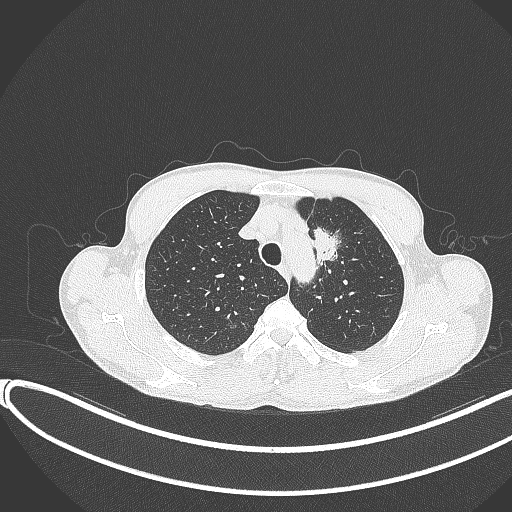
Chest CT, one axial slice. Slice 306 of 374 in the series (ordered by position). 120 kVp. Lung window (W 1500 / L -600 HU). 1 mm slice thickness. 512 × 512 image matrix. Male patient, age 58 years. From the clinical record (not read from this slice): clinical TNM (as recorded): T1c N1 M0.
Annotated regions visible in this slice (bounding box drawn by a radiologist):
- lung tumour (recorded histology: adenocarcinoma): bounding box <313,230,348,268> (left, top, right, bottom; pixels)